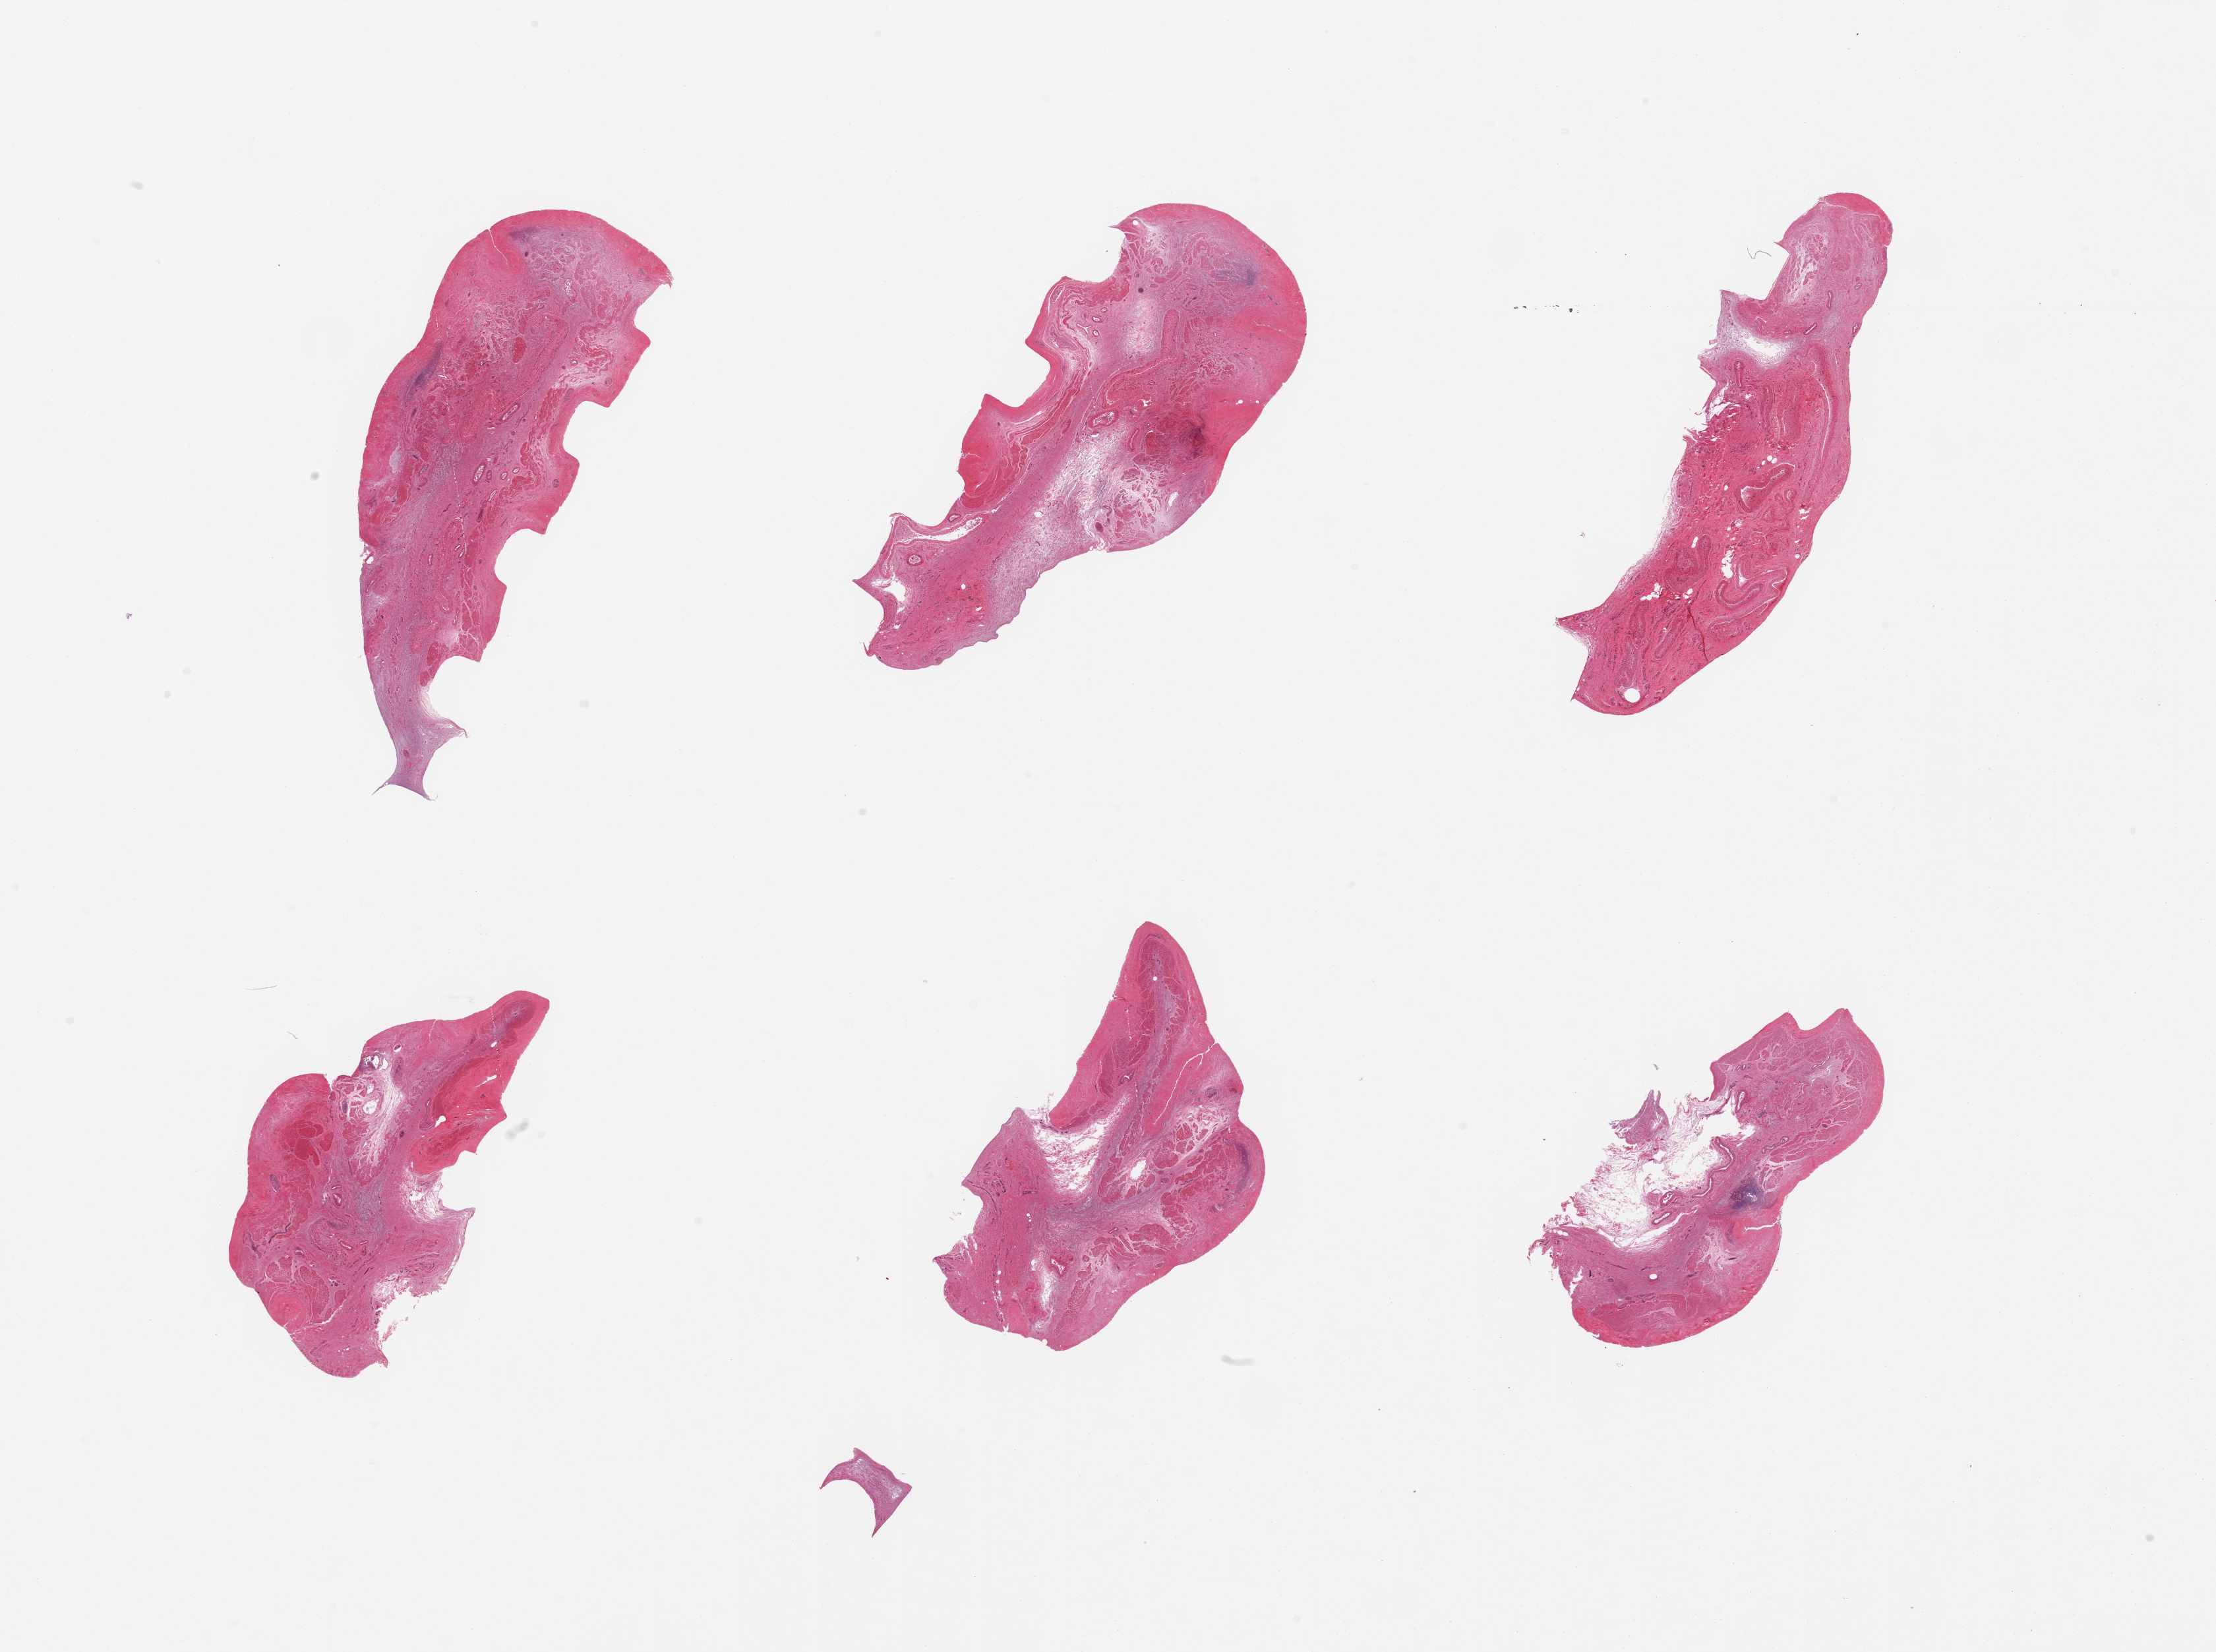
Digitized H&E-stained section, a low-resolution overview of the entire scanned area, about 26.6 x 19.8 mm, PAXgene-fixed paraffin-embedded (PFPE) section, section of esophageal mucous membrane (target tissue), tissue donor sample. Donor sex: male.
Review note (as recorded): 6 pieces; totally autolyzed.